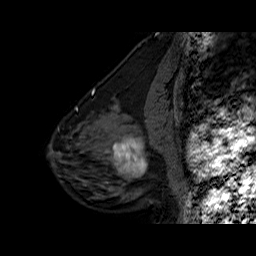
Breast MRI (dynamic contrast-enhanced), one sagittal slice; slice 23 of 60 in the series (ordered by position); dynamic contrast-enhanced series, time point 2 of 6 at this slice position (early post-contrast); 1.5 T; TE 6.3 ms, TR 32.5 ms; 4 mm slice thickness; 256 × 256 image matrix, field of view 200 × 200 mm. Female patient. From the clinical record (not read from this slice): setting: breast cancer imaged before/during neoadjuvant chemotherapy; receptor status: triple-negative.
Outlined on this slice (semi-automatically segmented with operator editing):
- analysis volume of interest (the breast-tissue region the enhancement analysis was run in; not a lesion): bounding box (x1, y1, x2, y2) in pixels: (102, 127, 162, 186)
- tumour enhancement mask (voxels above the 100 % enhancement threshold inside the analysis volume of interest): (105, 137, 148, 177)